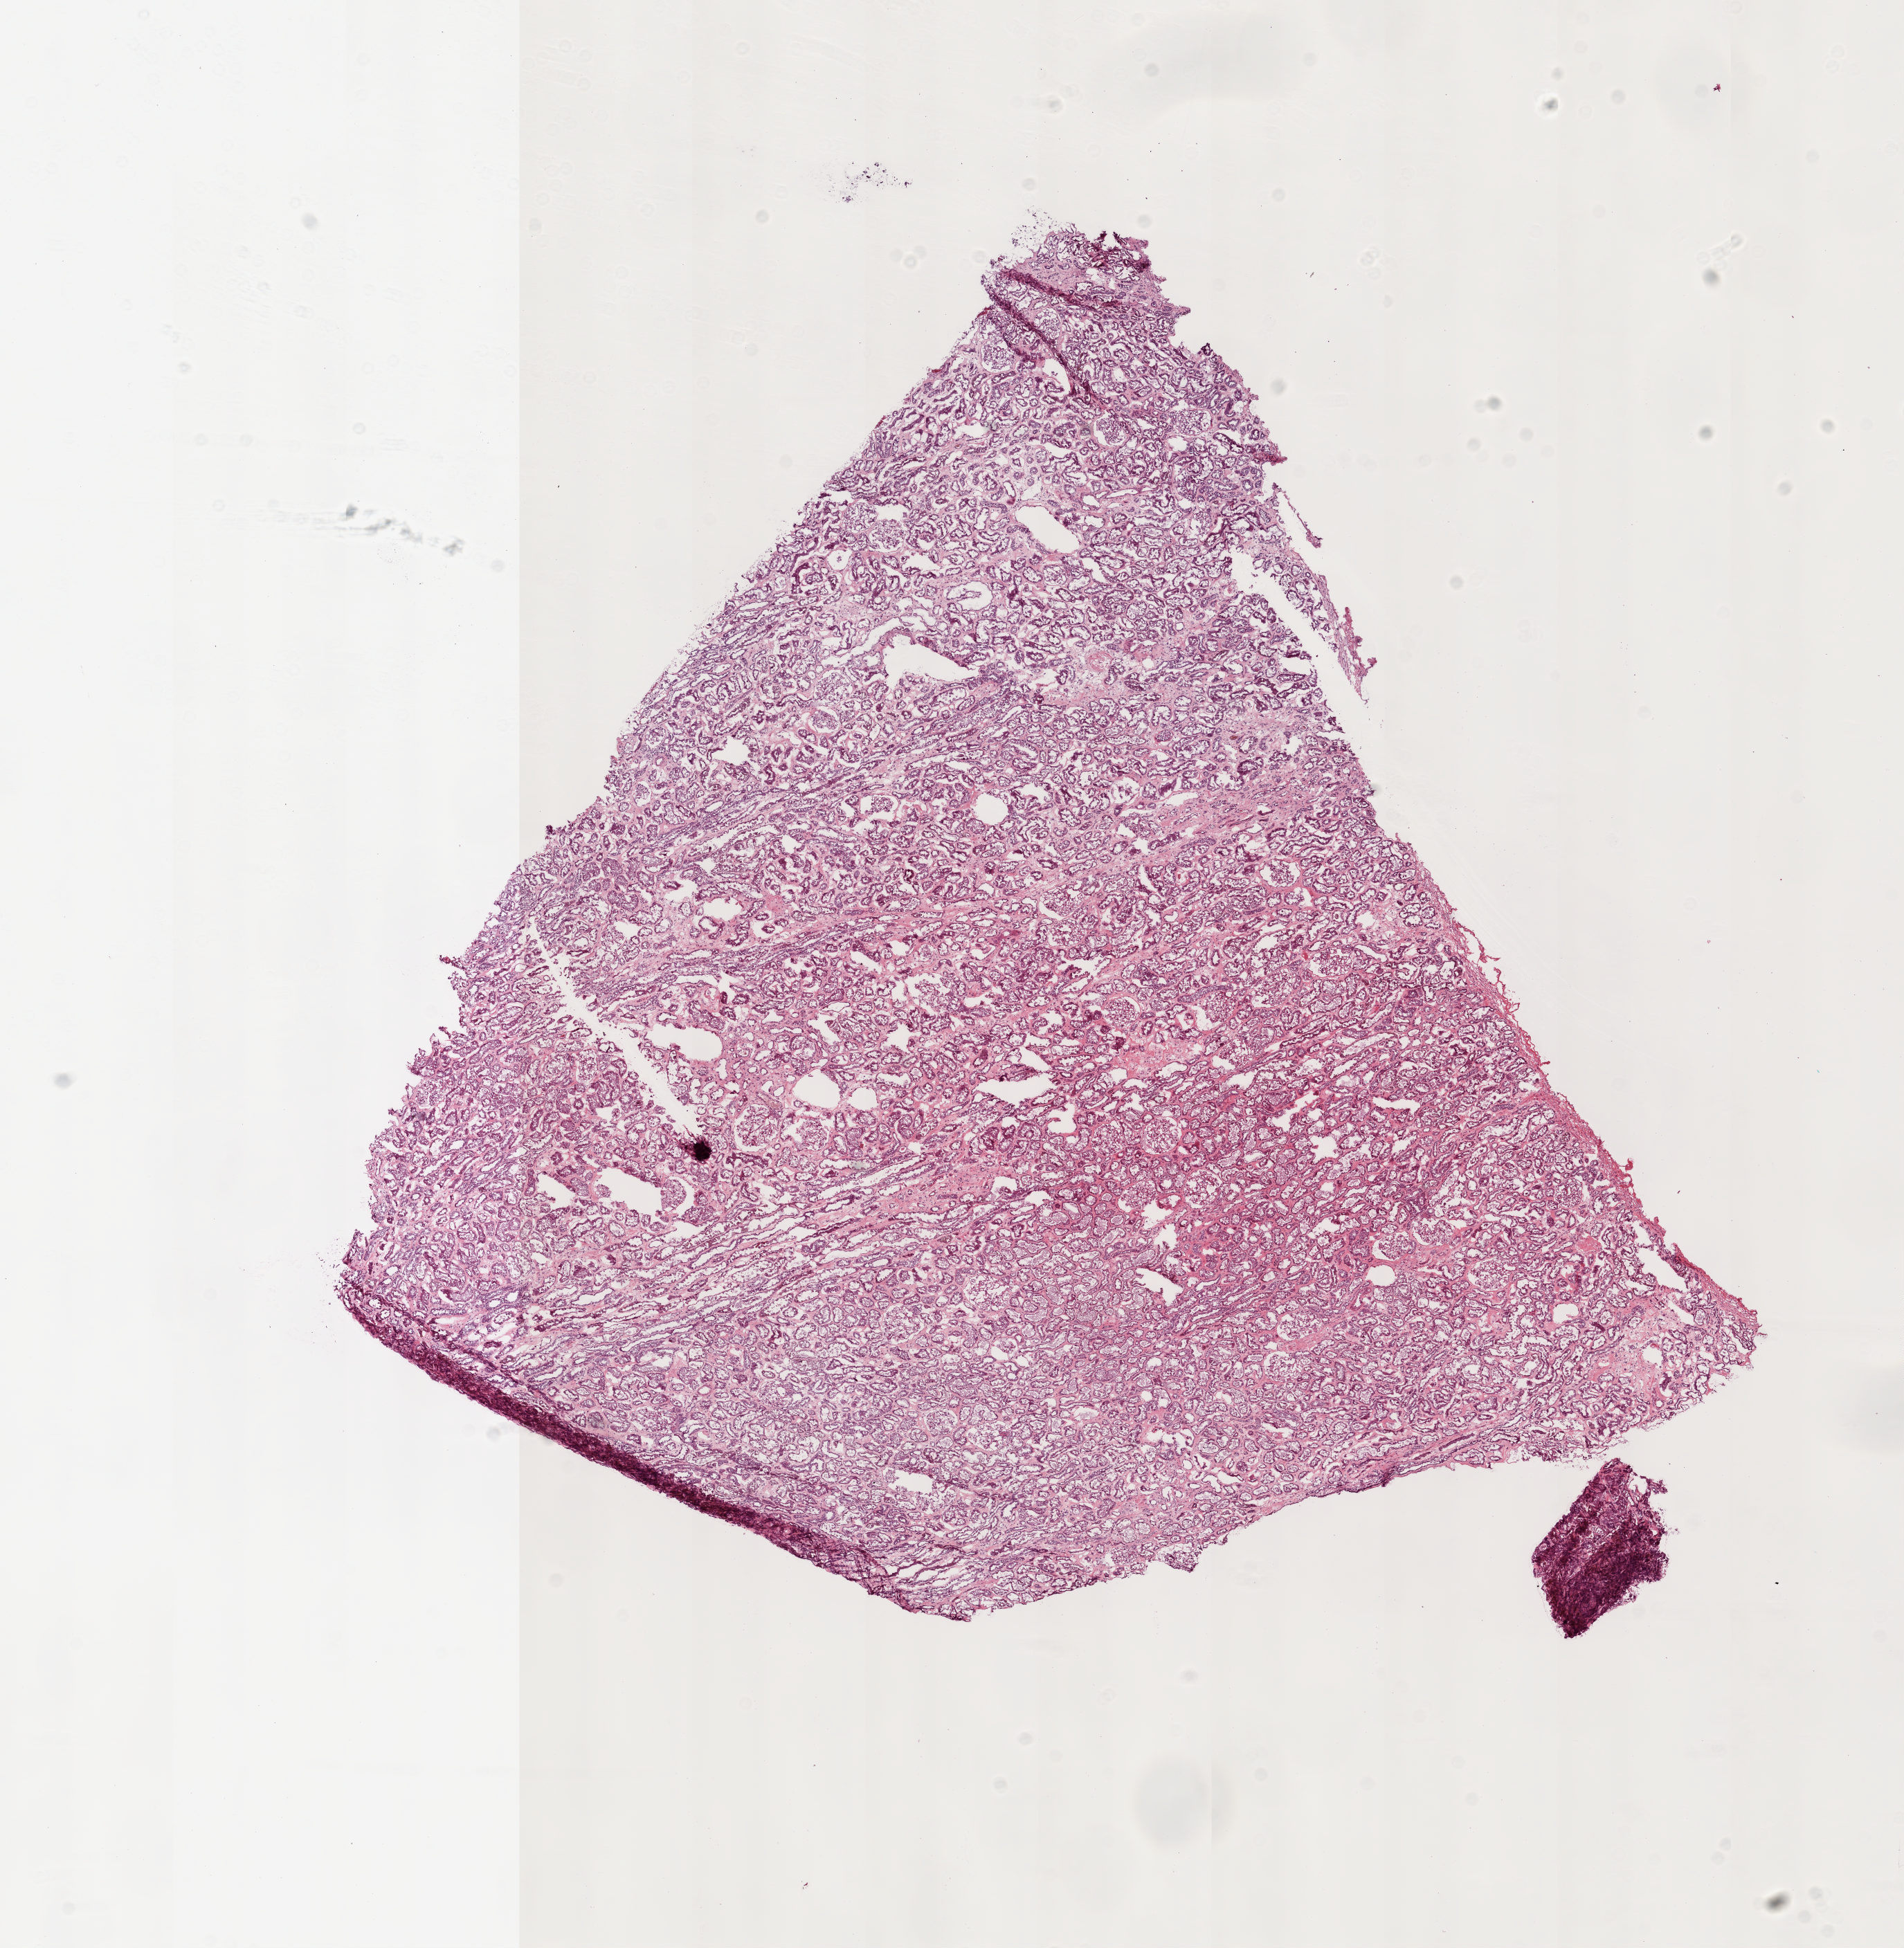
Digitized Hematoxylin and eosin (H&E) stained tissue section (whole slide), whole scanned area (about 10.9 x 11.2 mm, slide scanned at 20x) shown as a low-resolution overview, frozen section from the top of the tissue portion, sample: solid tissue normal (non-tumour tissue), kidney. Patient: male, age at initial diagnosis 74 years.
* this section: solid tissue normal sample (biorepository sample class)
* patient diagnosis: Clear cell adenocarcinoma, NOS